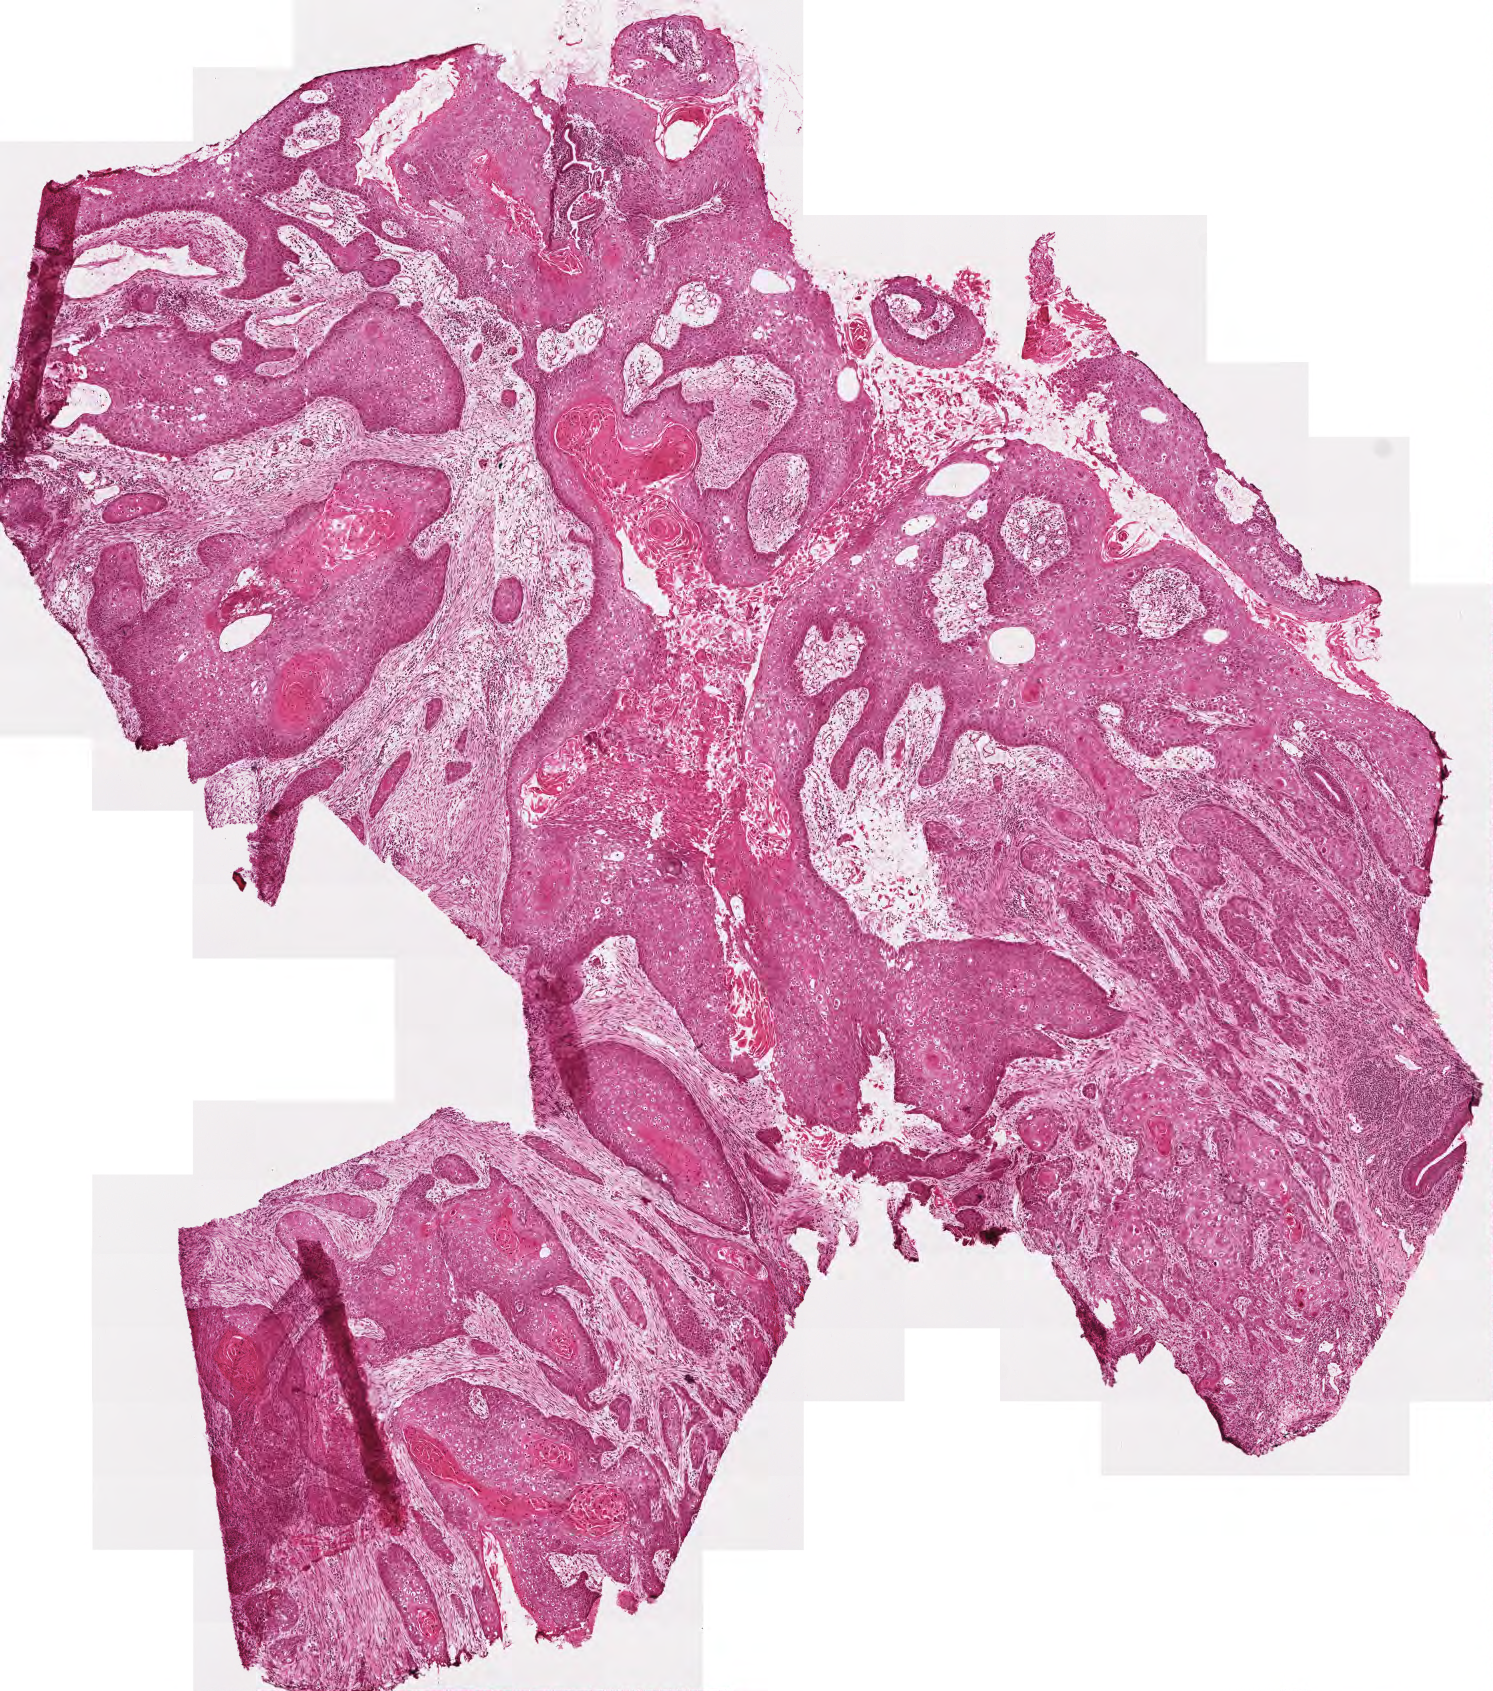
Digitized H&E tissue section (whole slide) — shown as a low-resolution overview of the whole scanned area (about 3.0 x 3.4 mm). Frozen section from the top of the tissue portion. Primary tumour sample from the head and neck. Male patient; age at initial diagnosis 52 years. Slide review estimates, as recorded: tumour cells 75%, tumour nuclei 60%.
Histologic diagnosis: Squamous cell carcinoma, NOS (overlapping lesion of lip, oral cavity and pharynx).